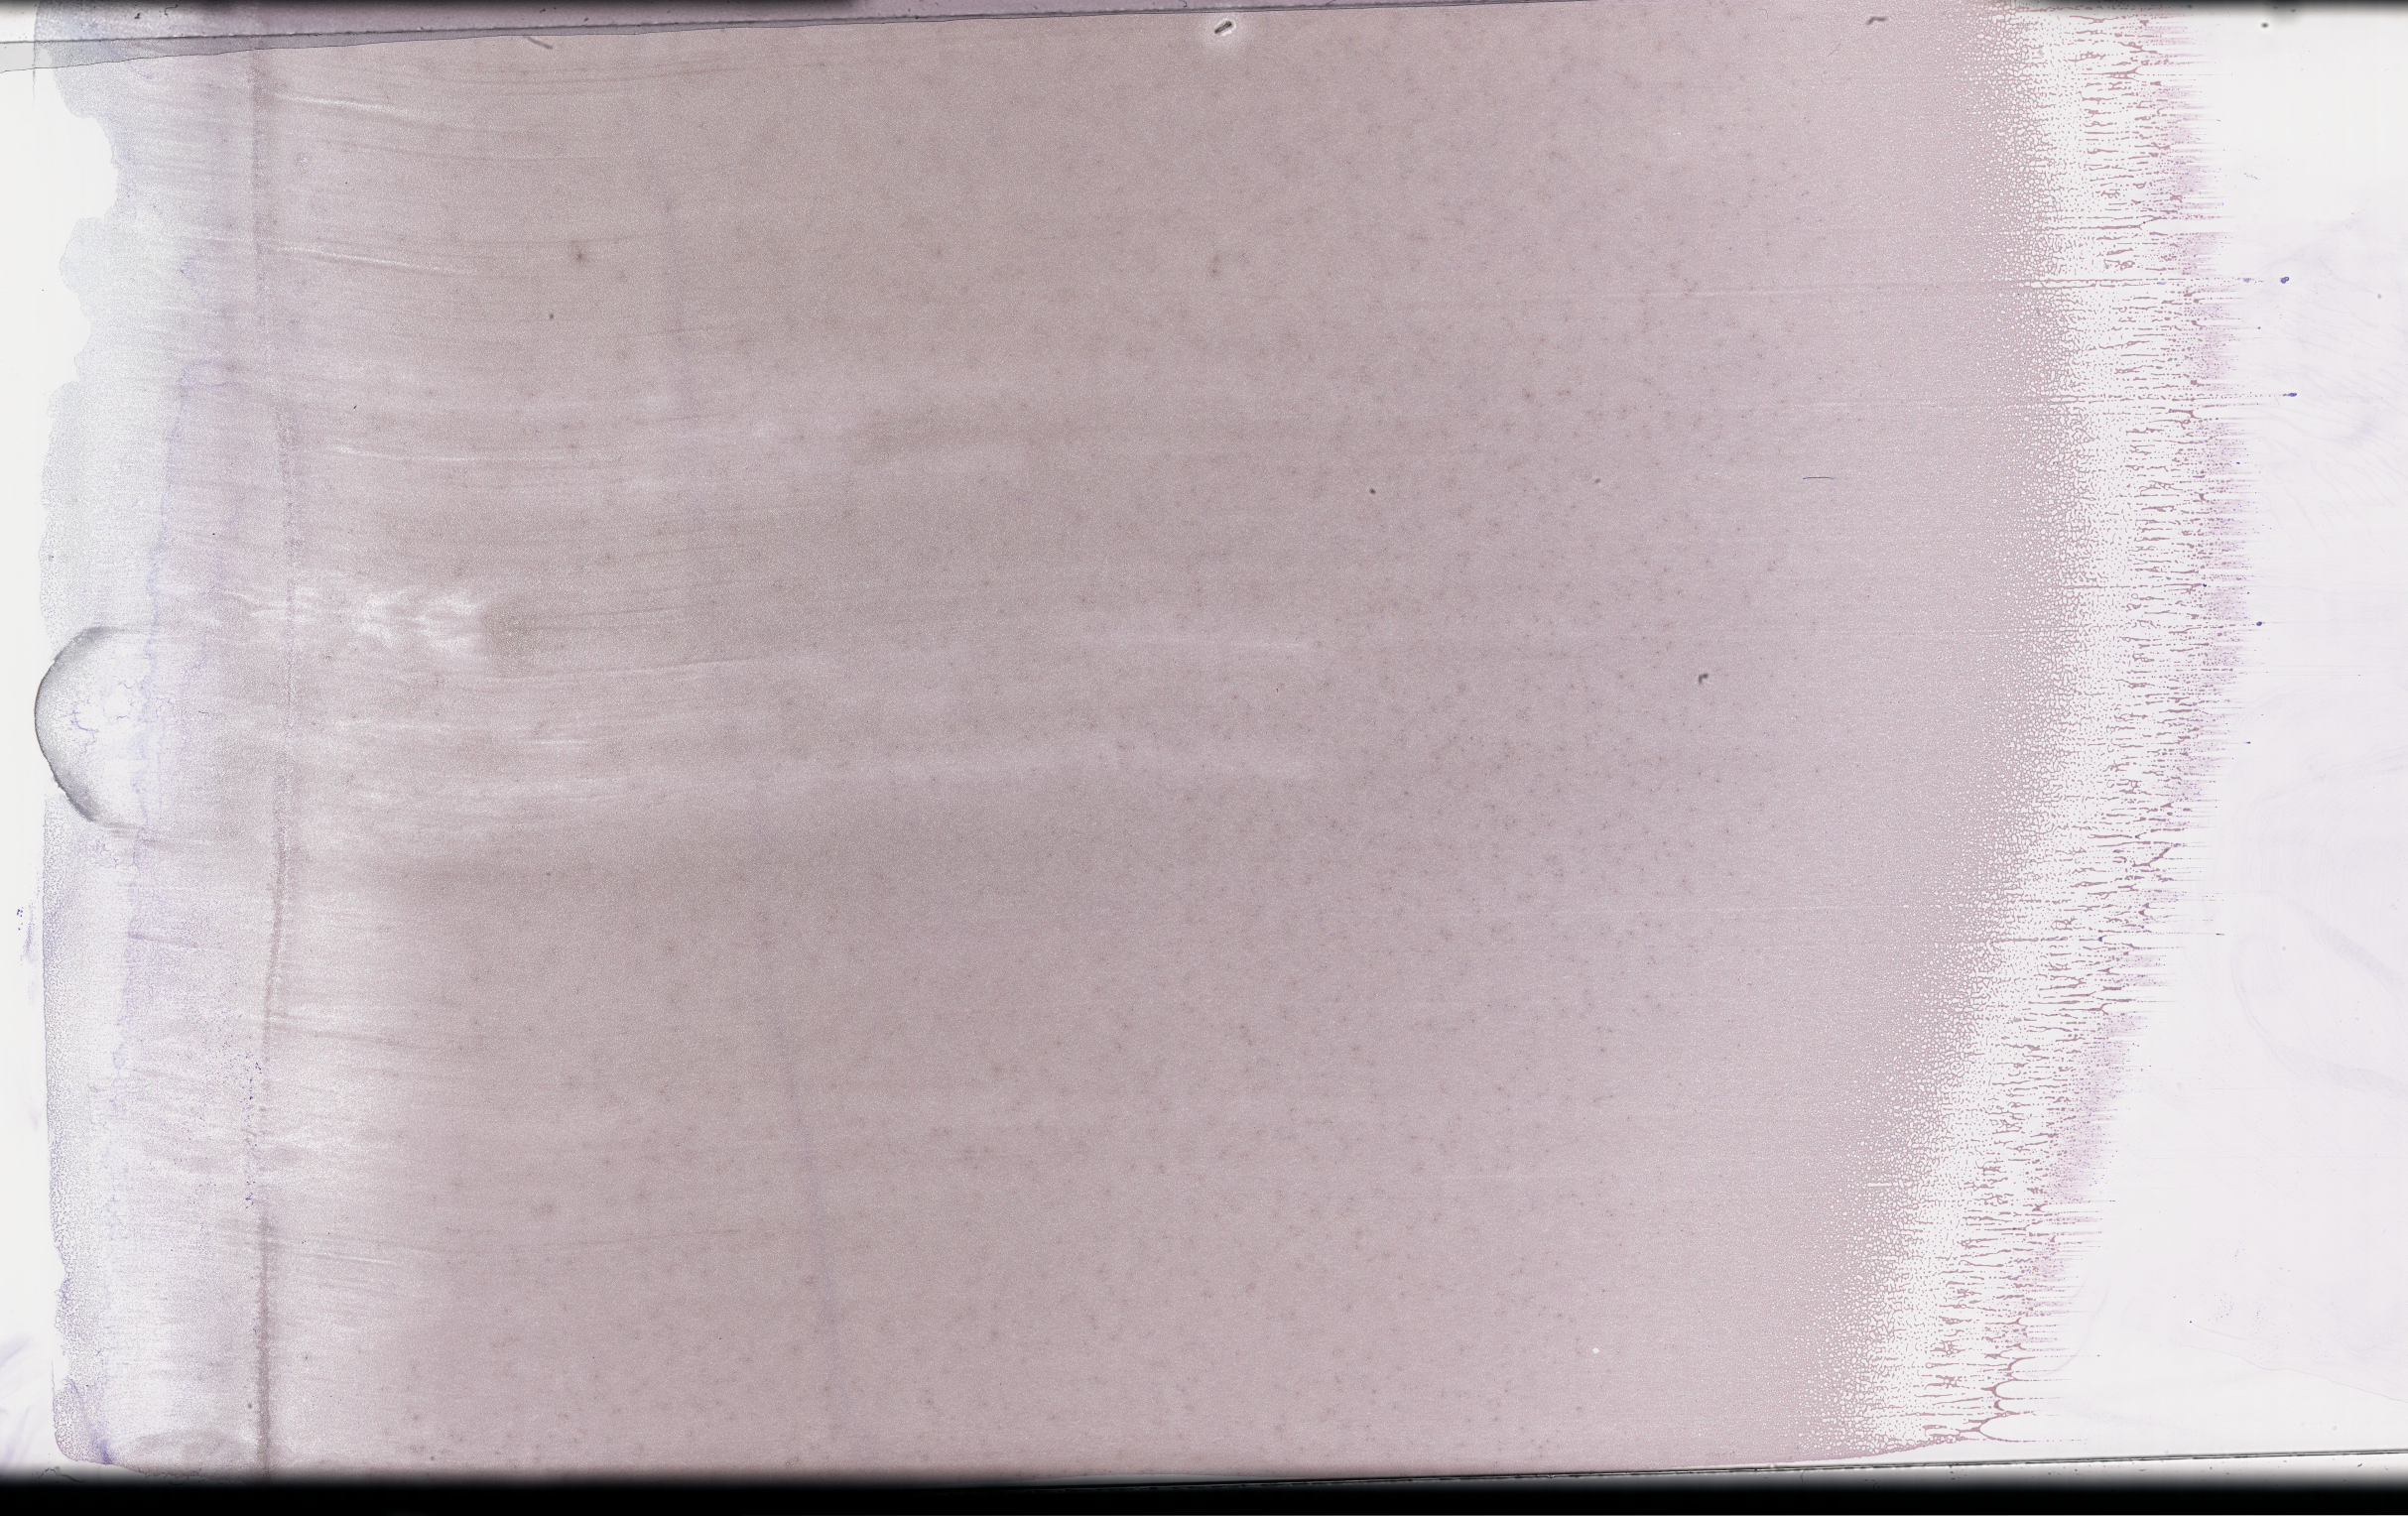
Wright–Giemsa-stained whole blood smear, whole-slide image, whole scanned area (about 39.2 x 24.7 mm) shown as a low-resolution overview. Male patient.
From a patient with: Plasma Cell Myeloma.